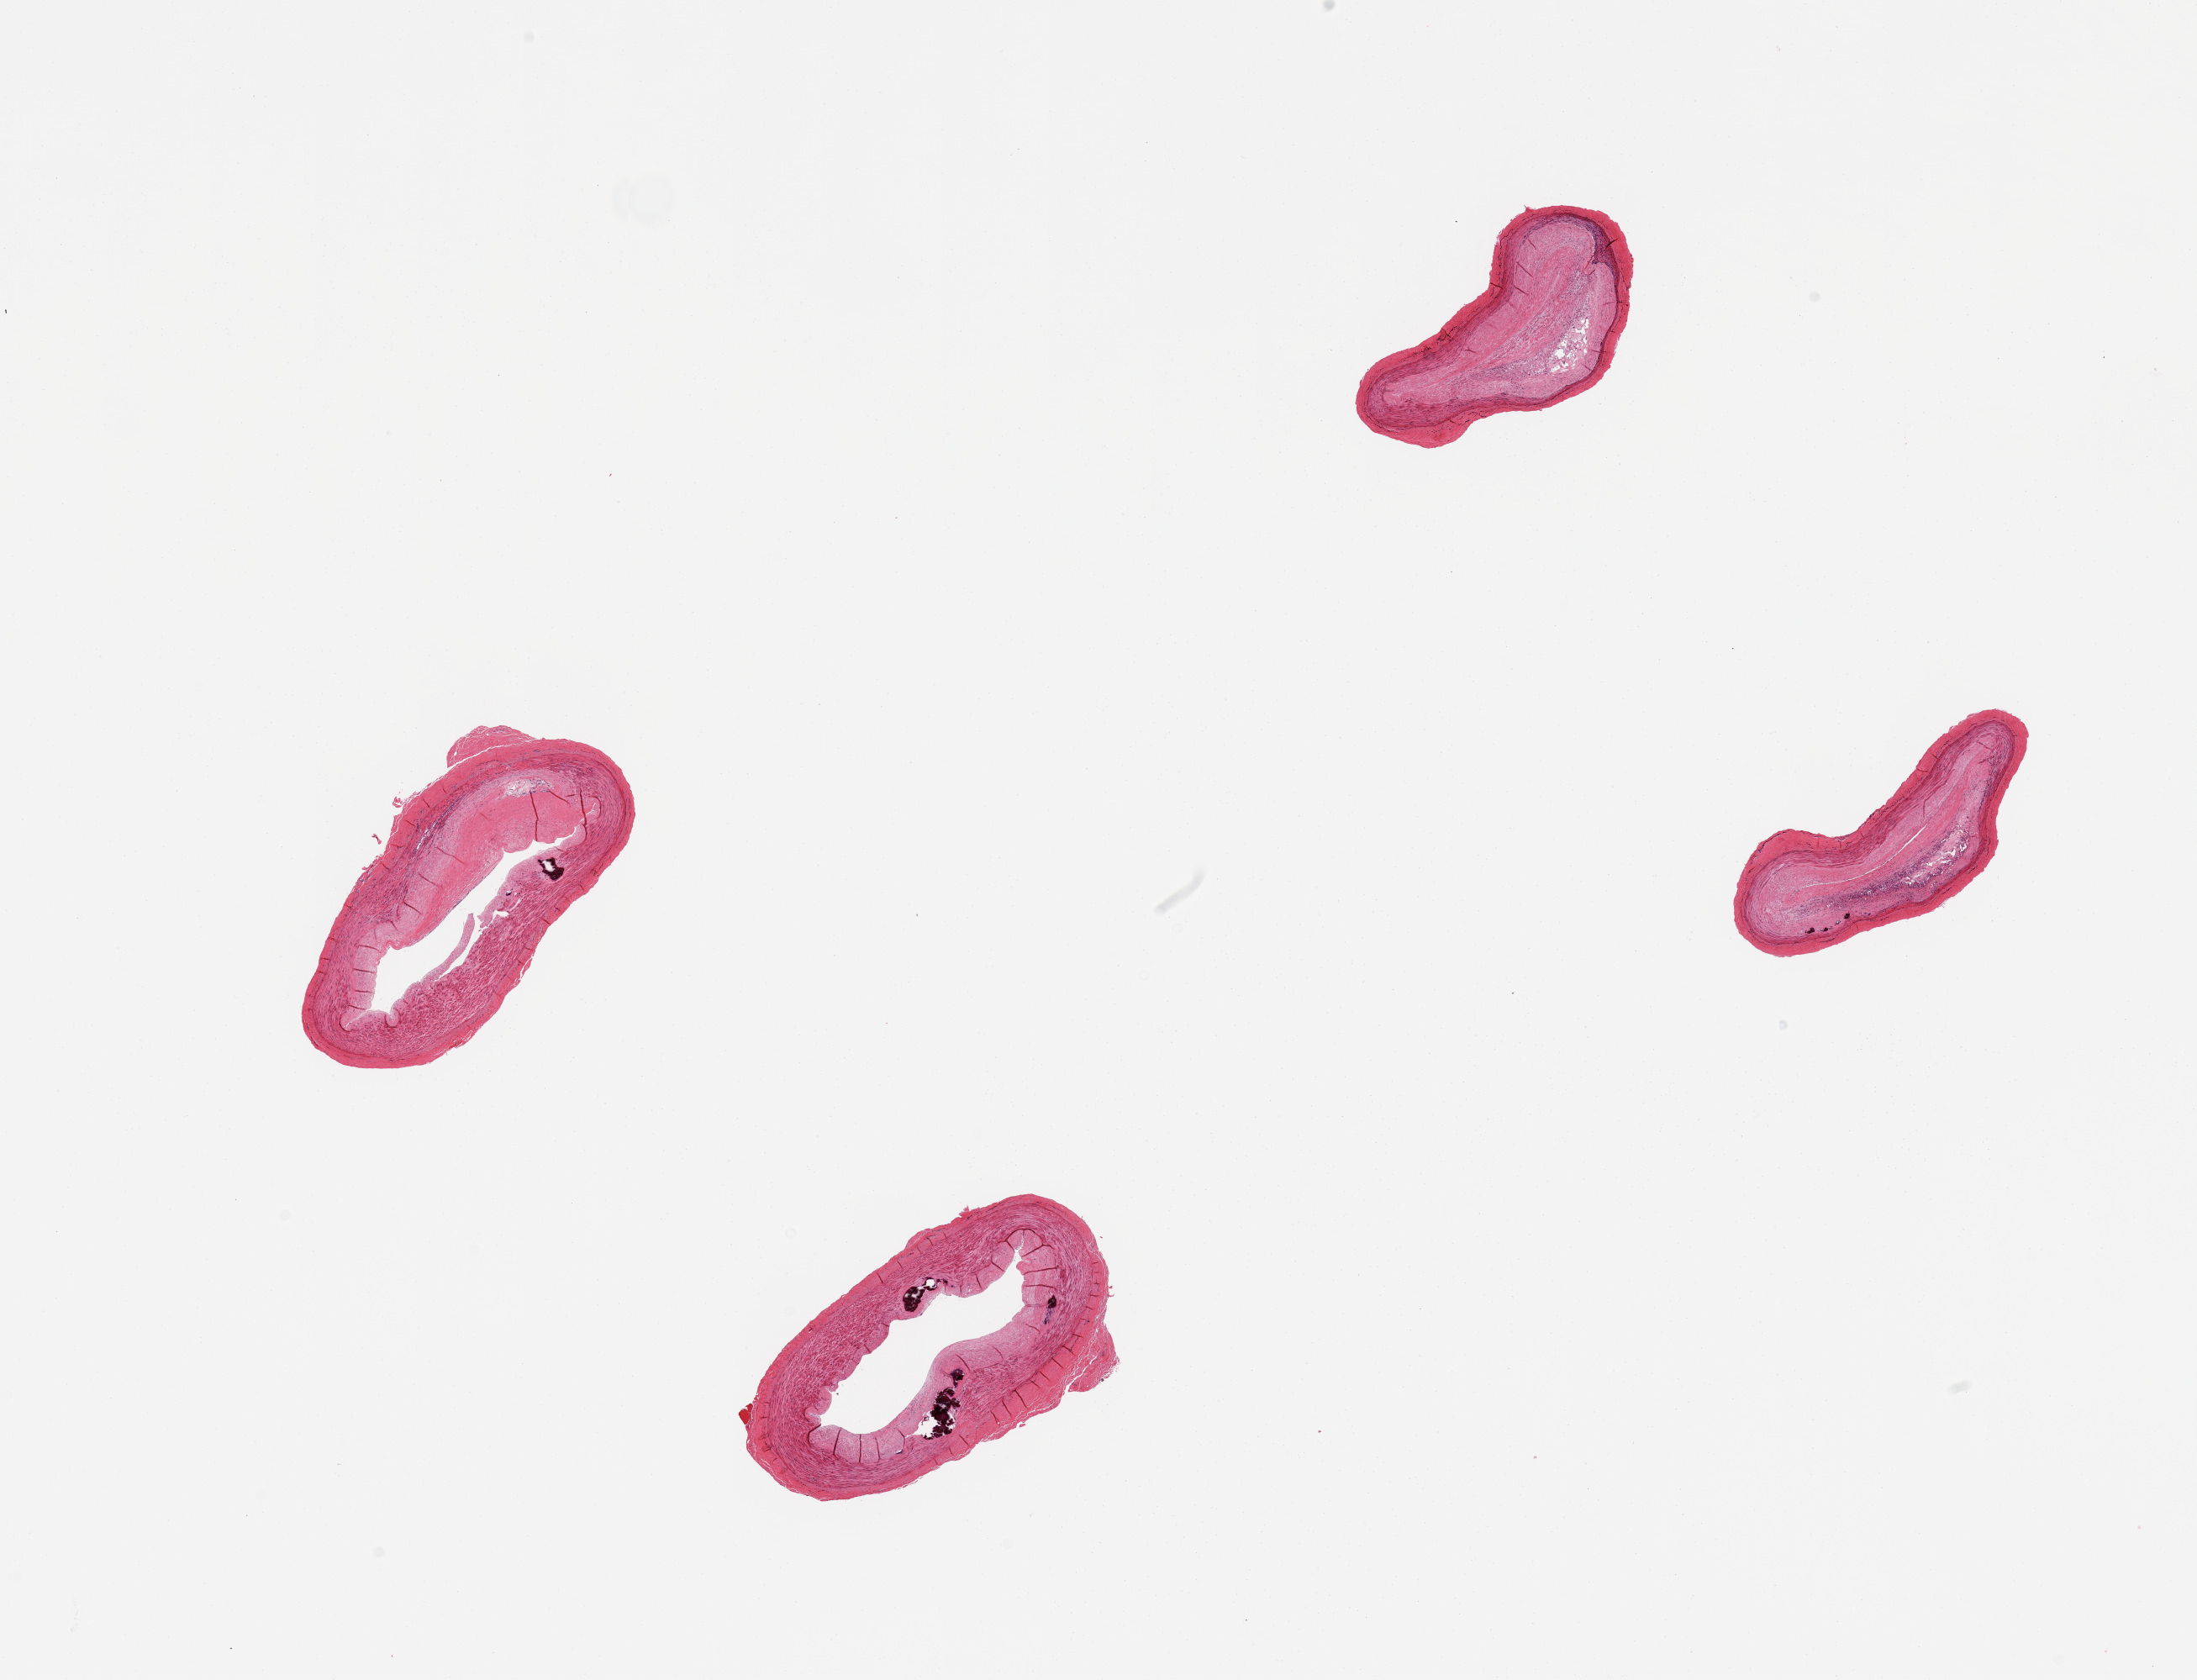
Whole-slide image, haematoxylin and eosin stain — whole scanned area (about 20.7 x 15.8 mm) shown as a low-resolution overview, PAXgene-fixed paraffin-embedded (PFPE) section, target tissue: tibial artery, donor tissue sample. Male donor.
* pathologist's review note for this sample: 4 pieces; mural calcifications; well trimmed